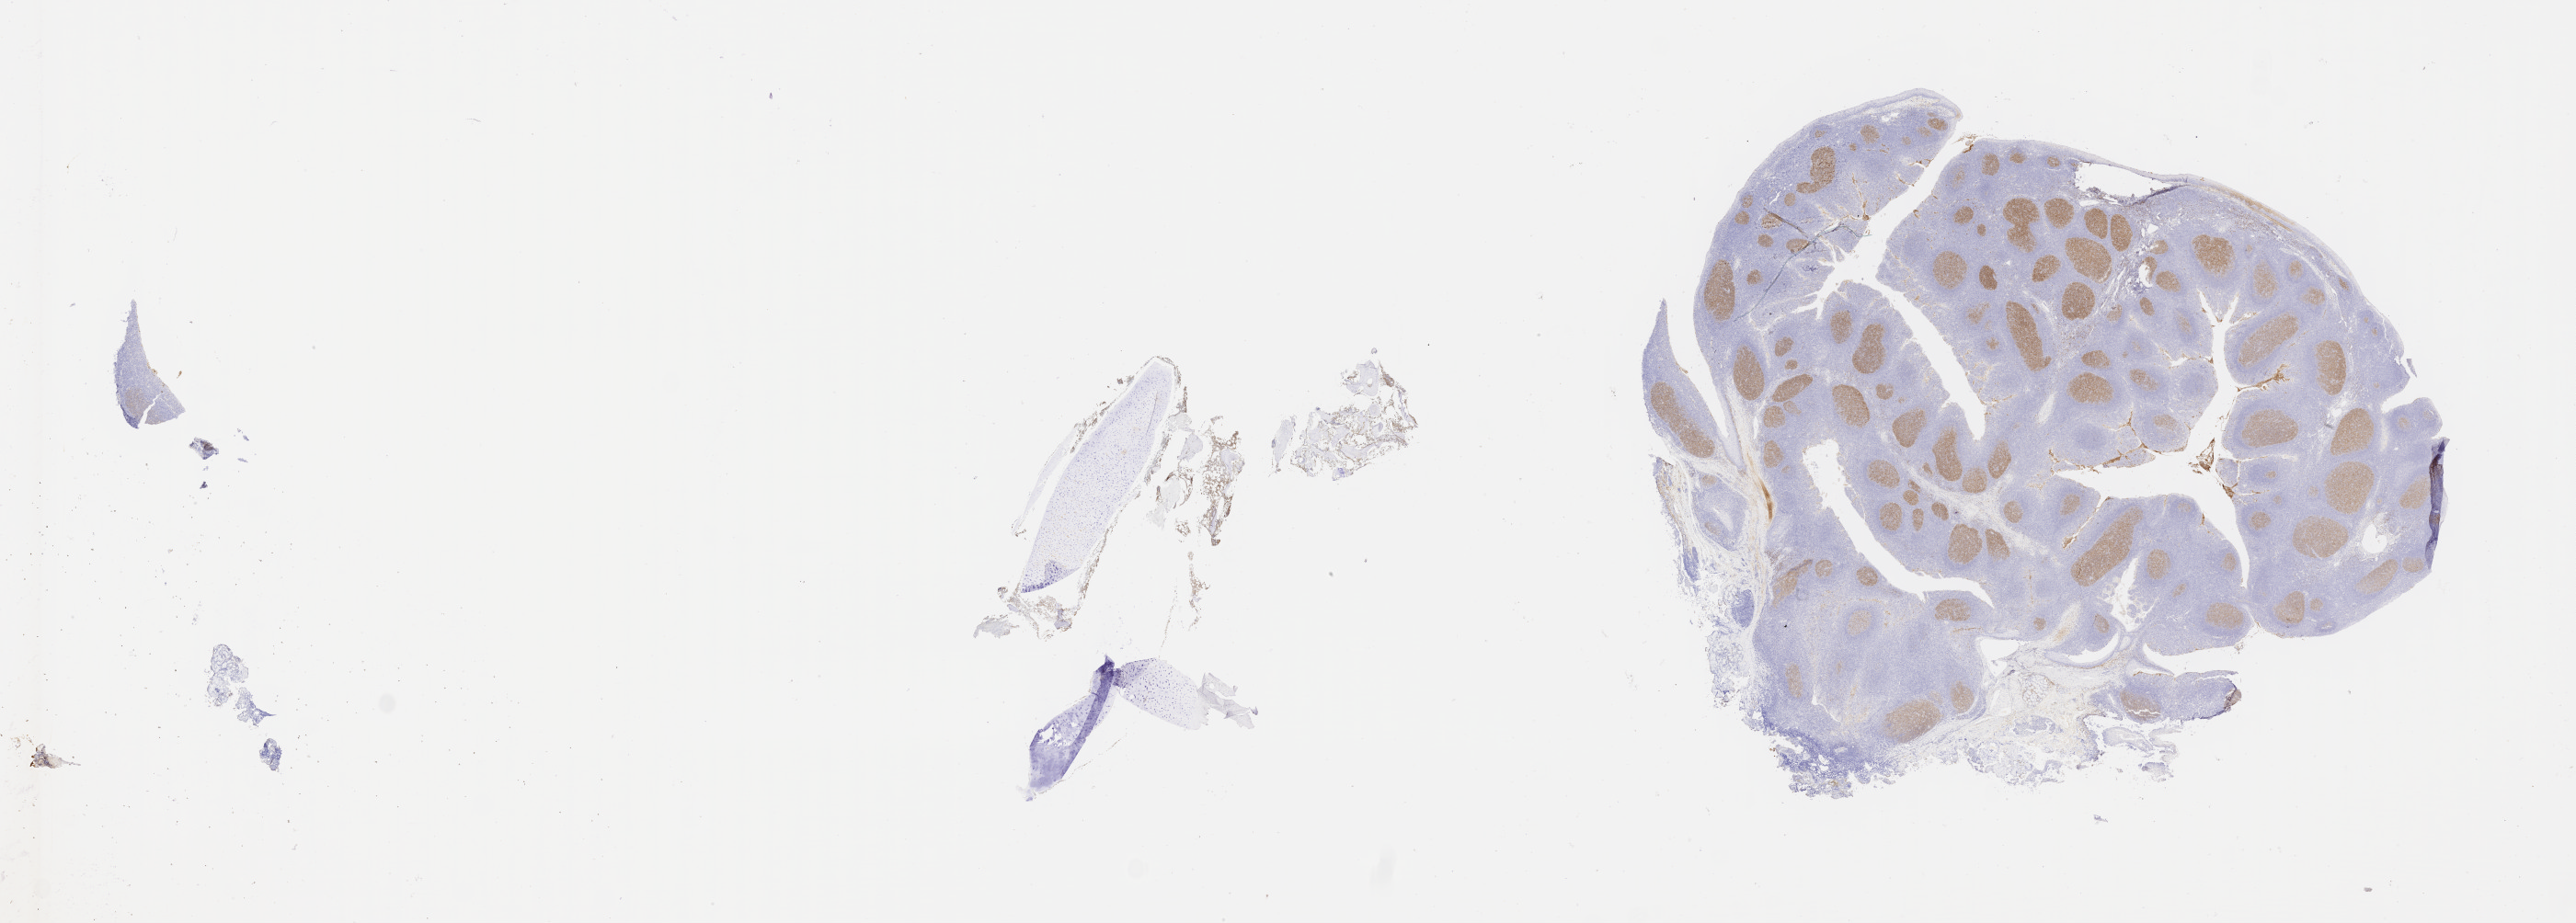
IHC for CD10, whole-slide image, low-resolution overview of the scanned area, about 45.3 x 16.2 mm; tumor tissue; anatomic site: bone marrow. Patient: female, 11 years old.
Histologic diagnosis: Burkitt lymphoma, NOS.